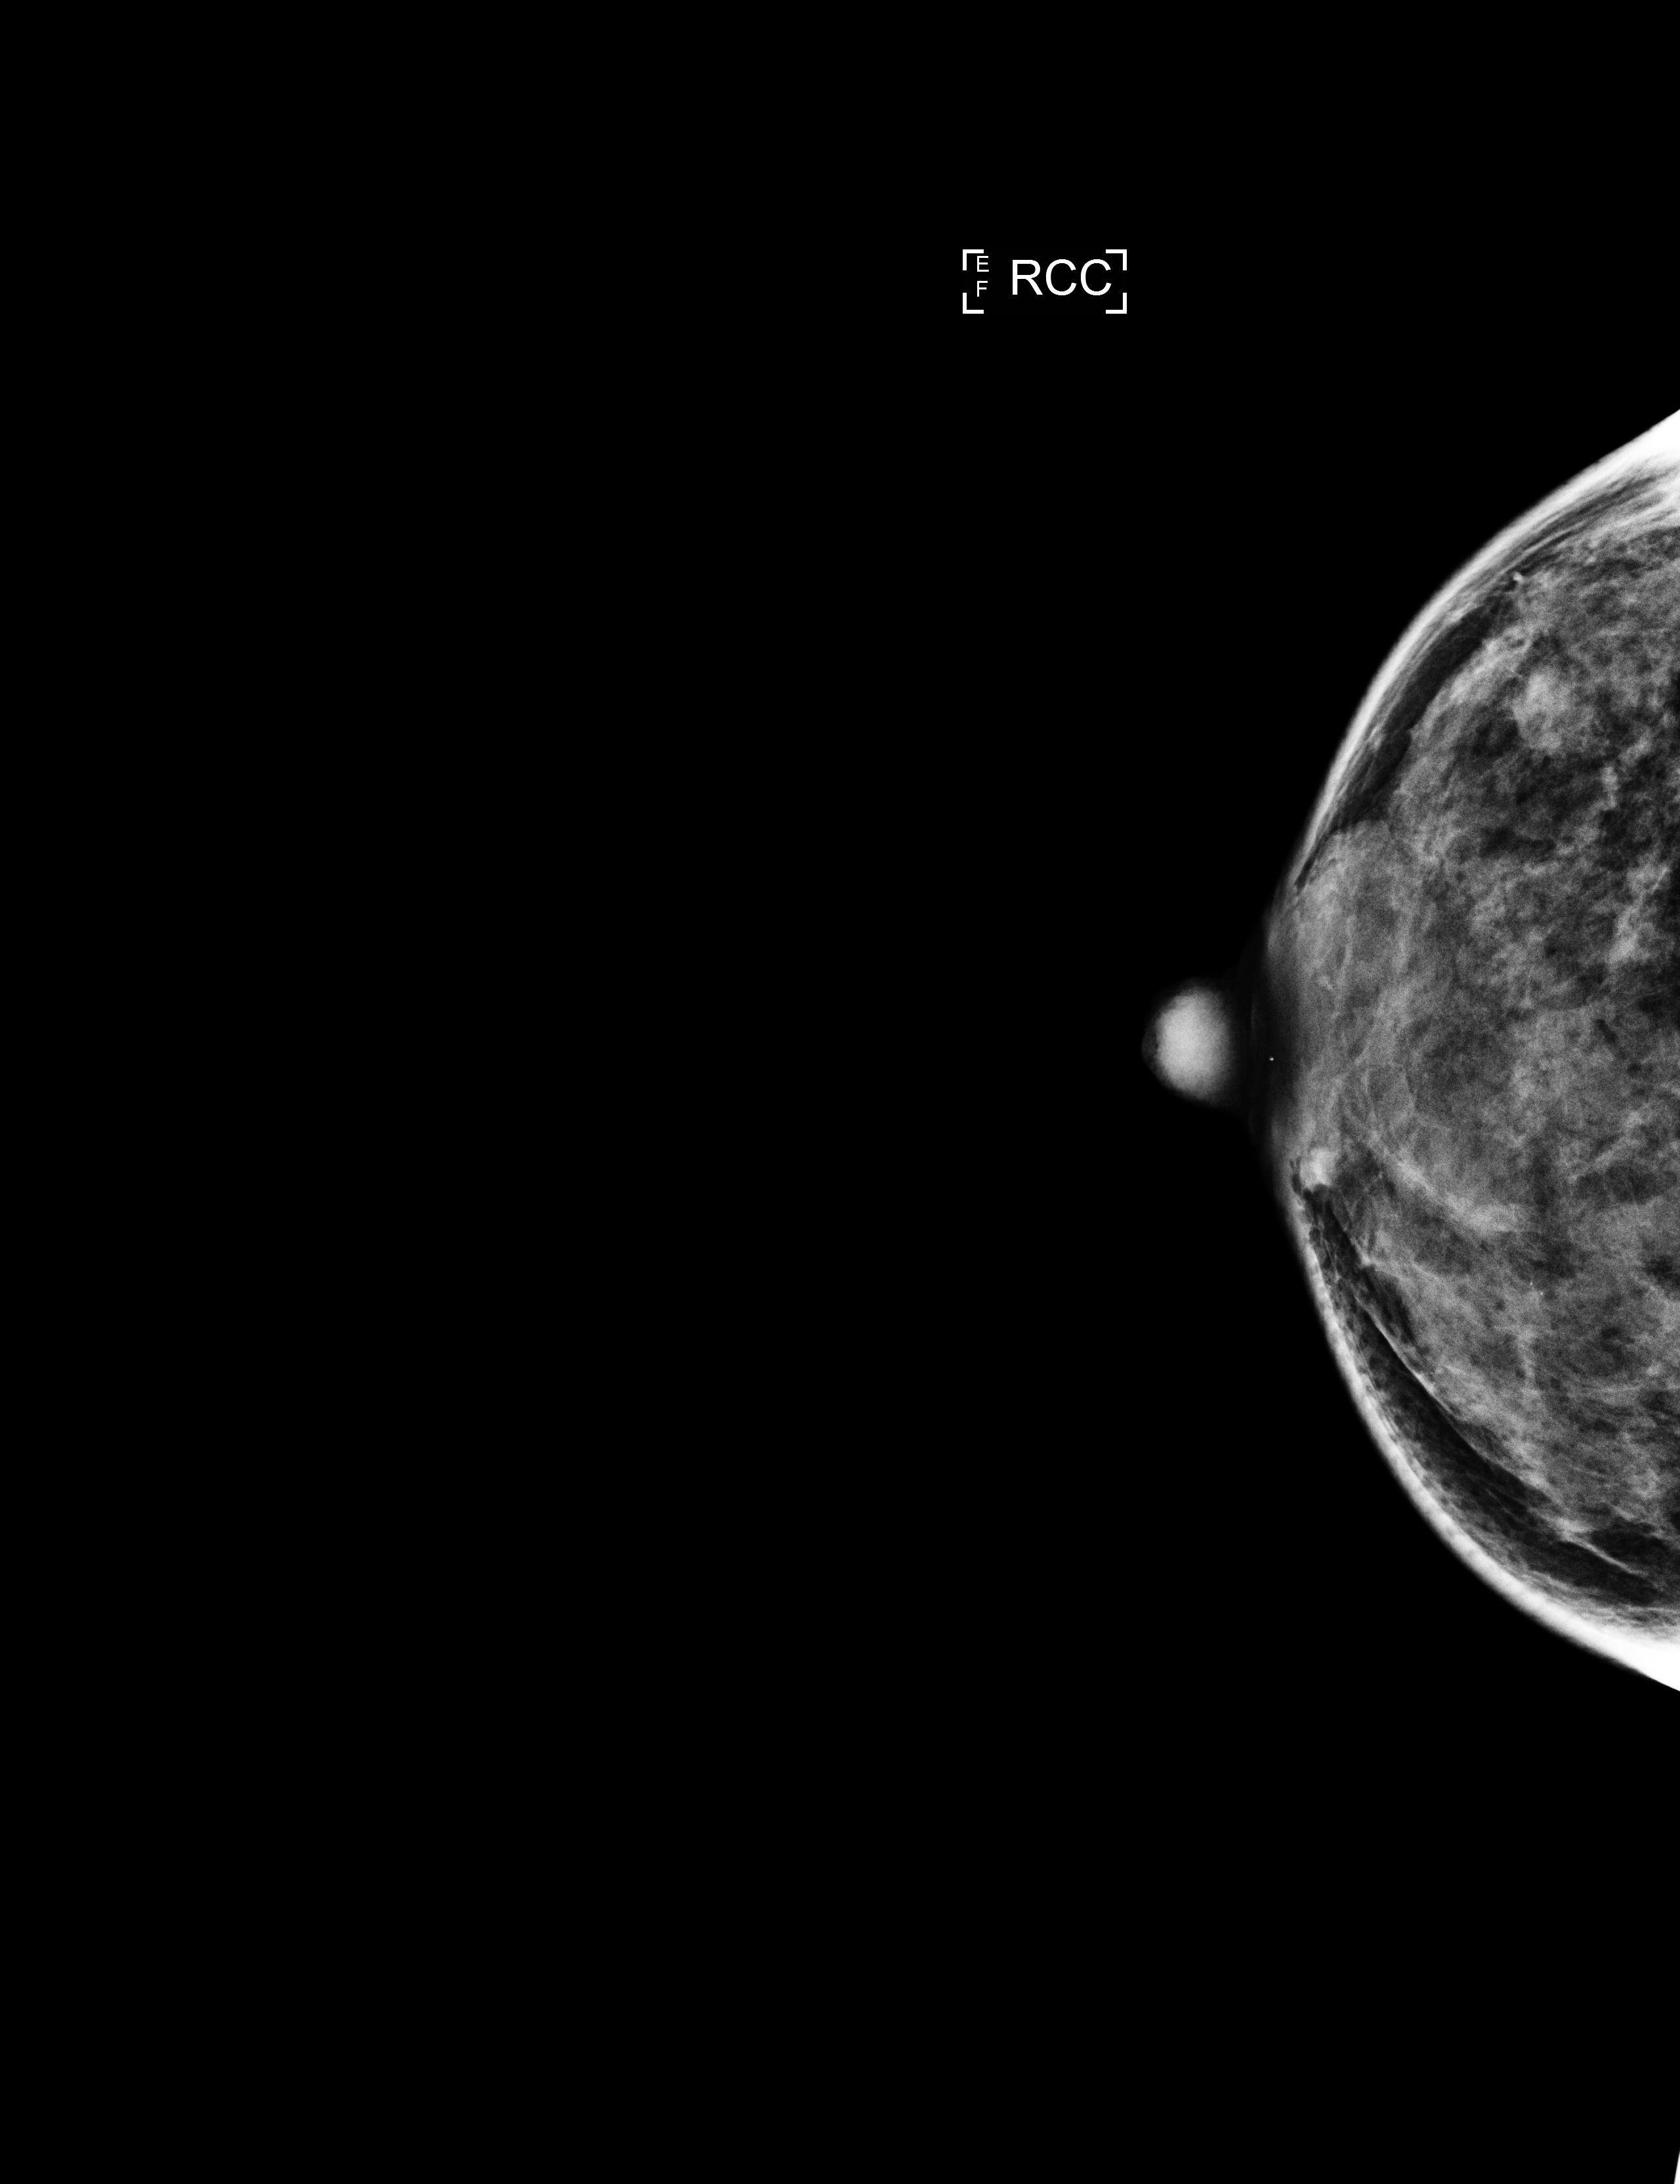
Full-field digital mammogram (FFDM); right breast; craniocaudal (CC) view; annual screening mammography examination; compressed breast thickness 33 mm. Female patient, age 59 years.
- breast density at the screening exam (both breasts): heterogeneously dense (BI-RADS density category c)
- final BI-RADS assessment for this screening round (tomosynthesis exam, both breasts): category 2
- recall: no recall after this screen